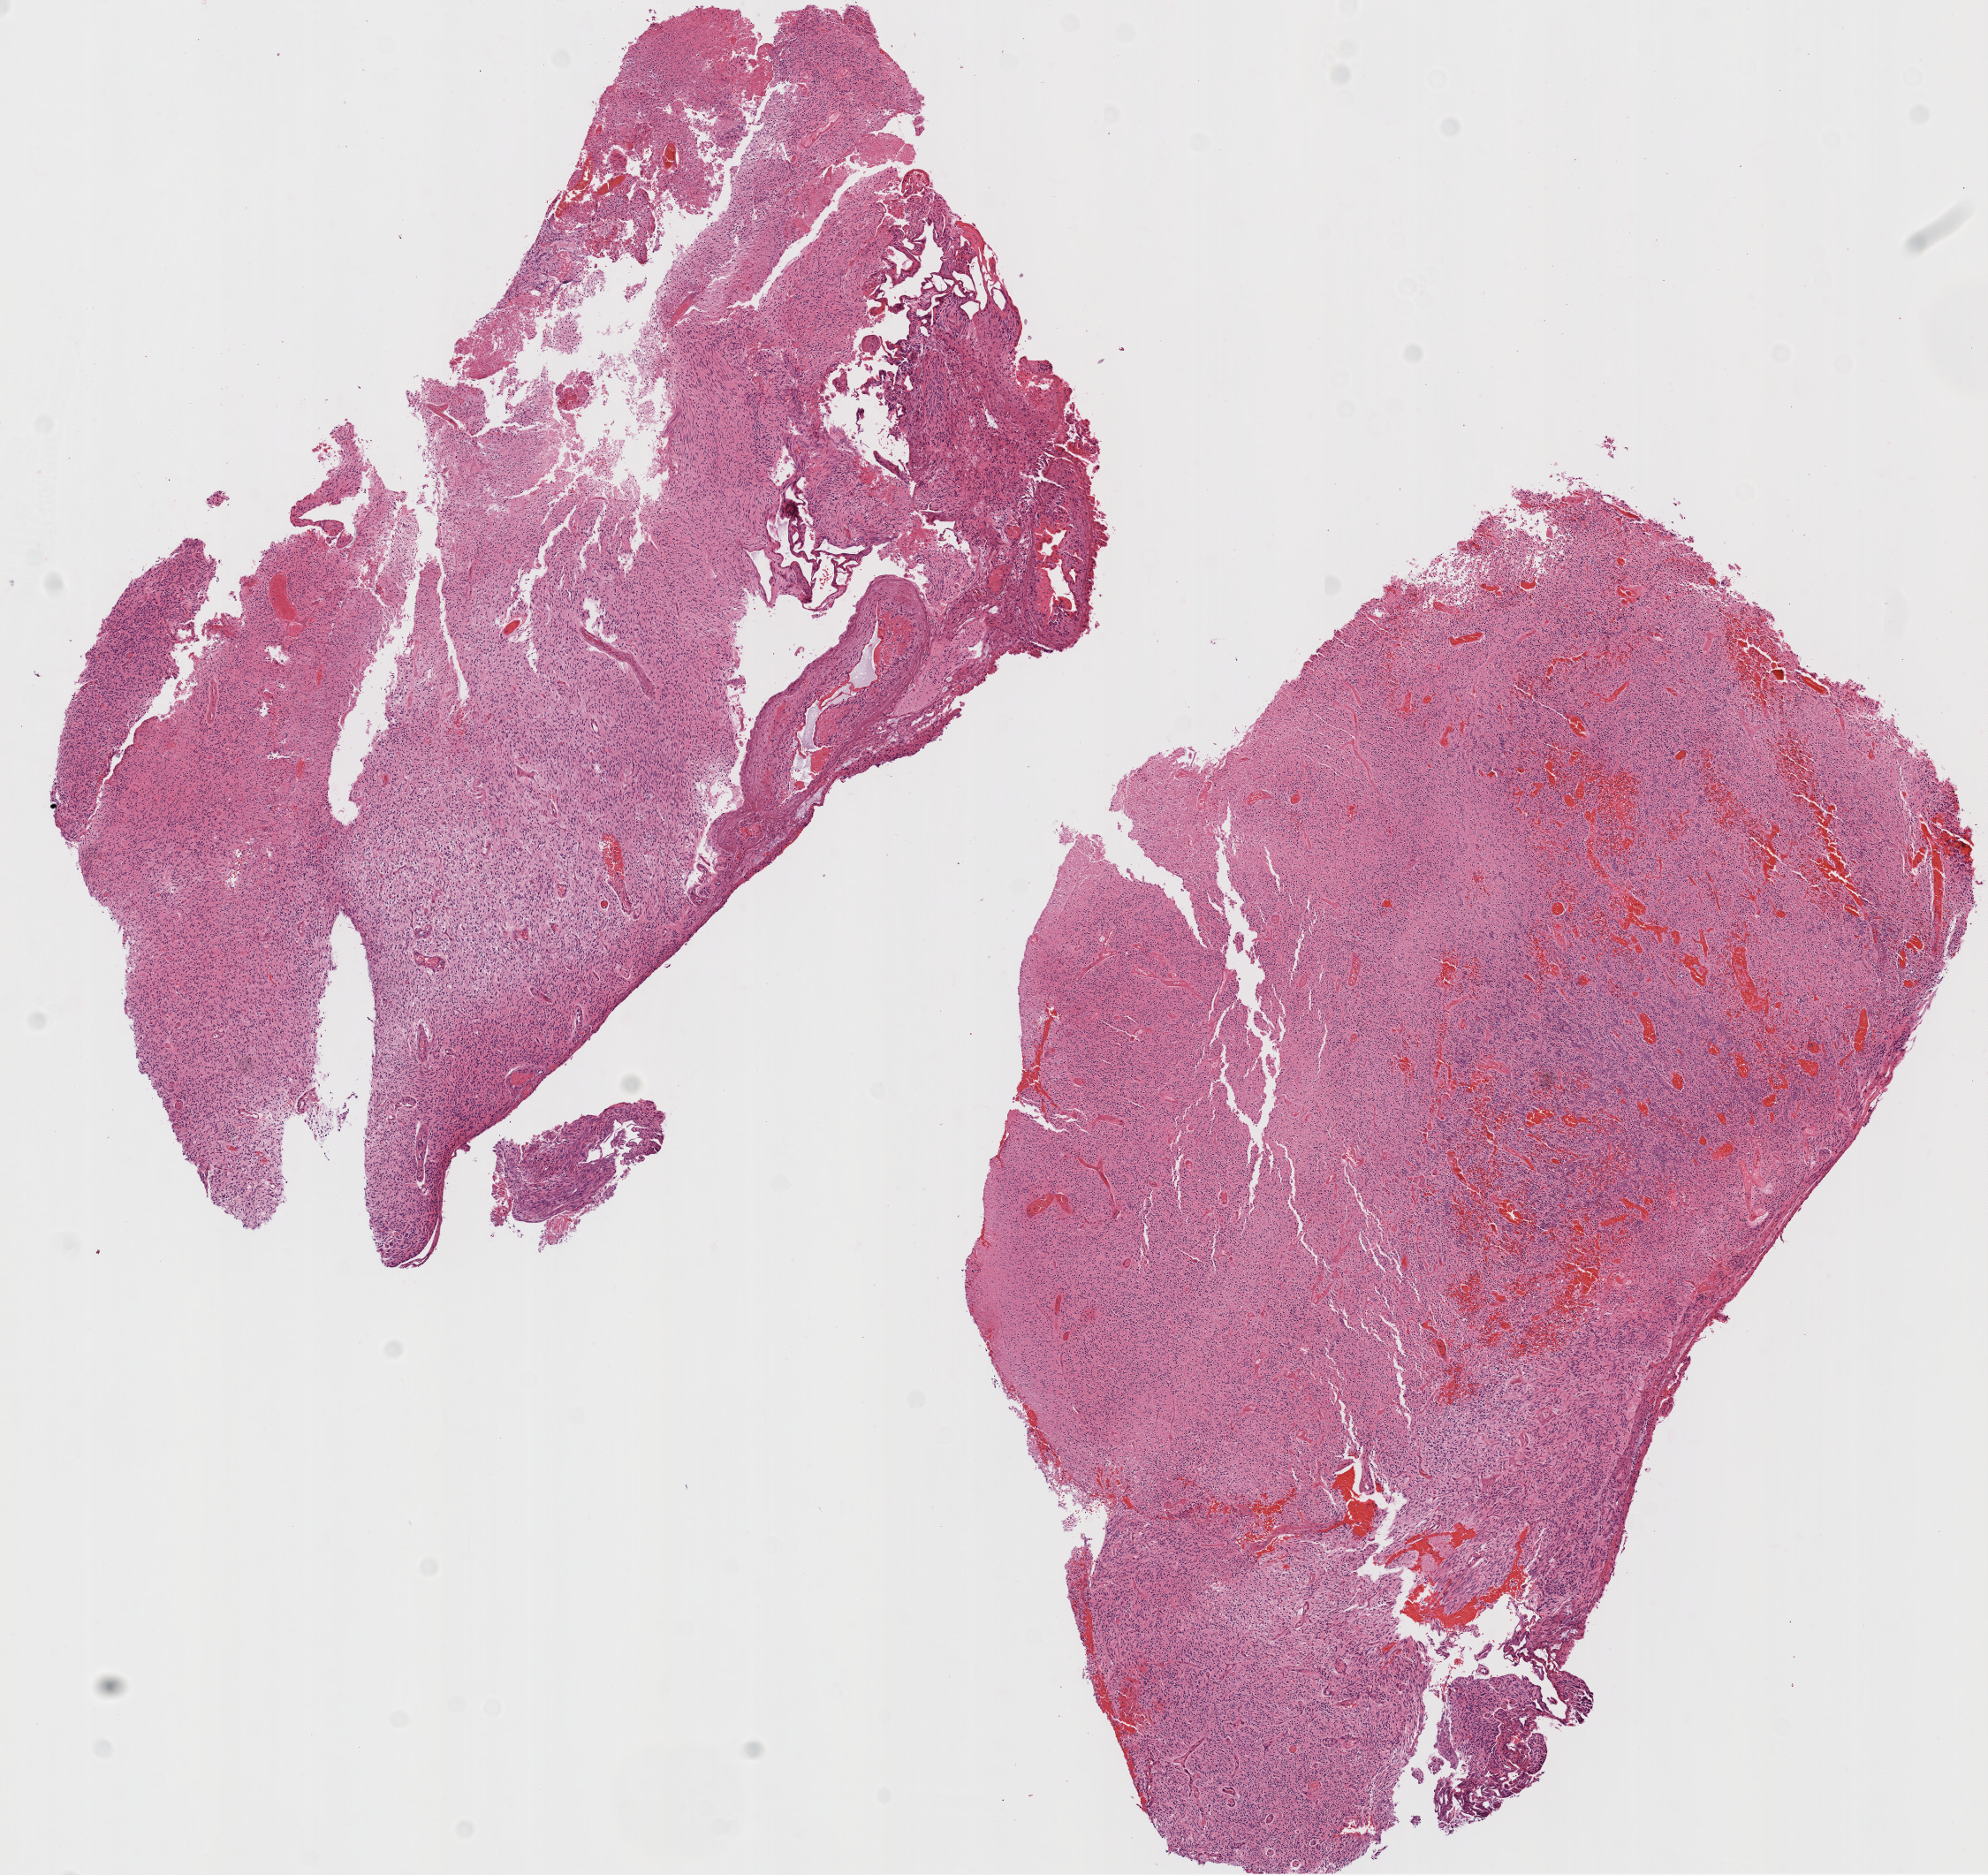
Whole-slide histology image, H&E-stained — shown as a low-resolution overview of the whole scanned area (about 9.0 x 8.5 mm, acquisition: 20x scan); formalin-fixed paraffin-embedded (FFPE) diagnostic section; sample: primary tumour, brain. Male patient; age at initial diagnosis 76 years.
Pathologic diagnosis: Glioblastoma.